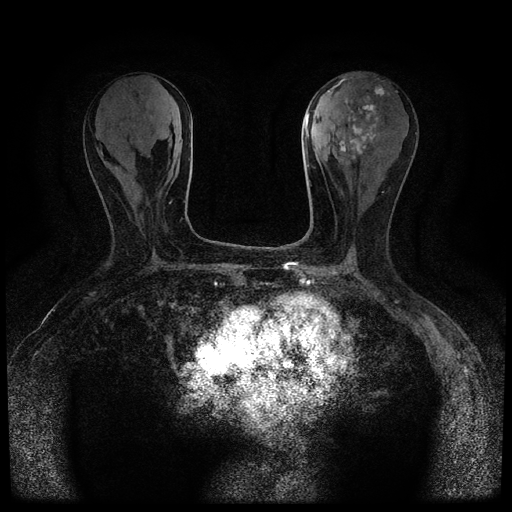
Breast MRI (dynamic contrast-enhanced, multi-phase), one axial slice; position 35 of 116 along the scan axis; dynamic contrast-enhanced series, time point 2 of 5 at this slice position (early post-contrast); 1.5 T; TE 2.7 ms, TR 5.4 ms; 512 × 512 image matrix, field of view 320 × 320 mm. Female patient, age 80 years.
Outlined on this slice (semi-automatic segmentation, software-assisted and operator-edited):
- breast lesion (labelled 'tumour' in the annotation; benign lesions carry a separate 'benign' label): bounding box [x1, y1, x2, y2] px = [339, 85, 384, 168]